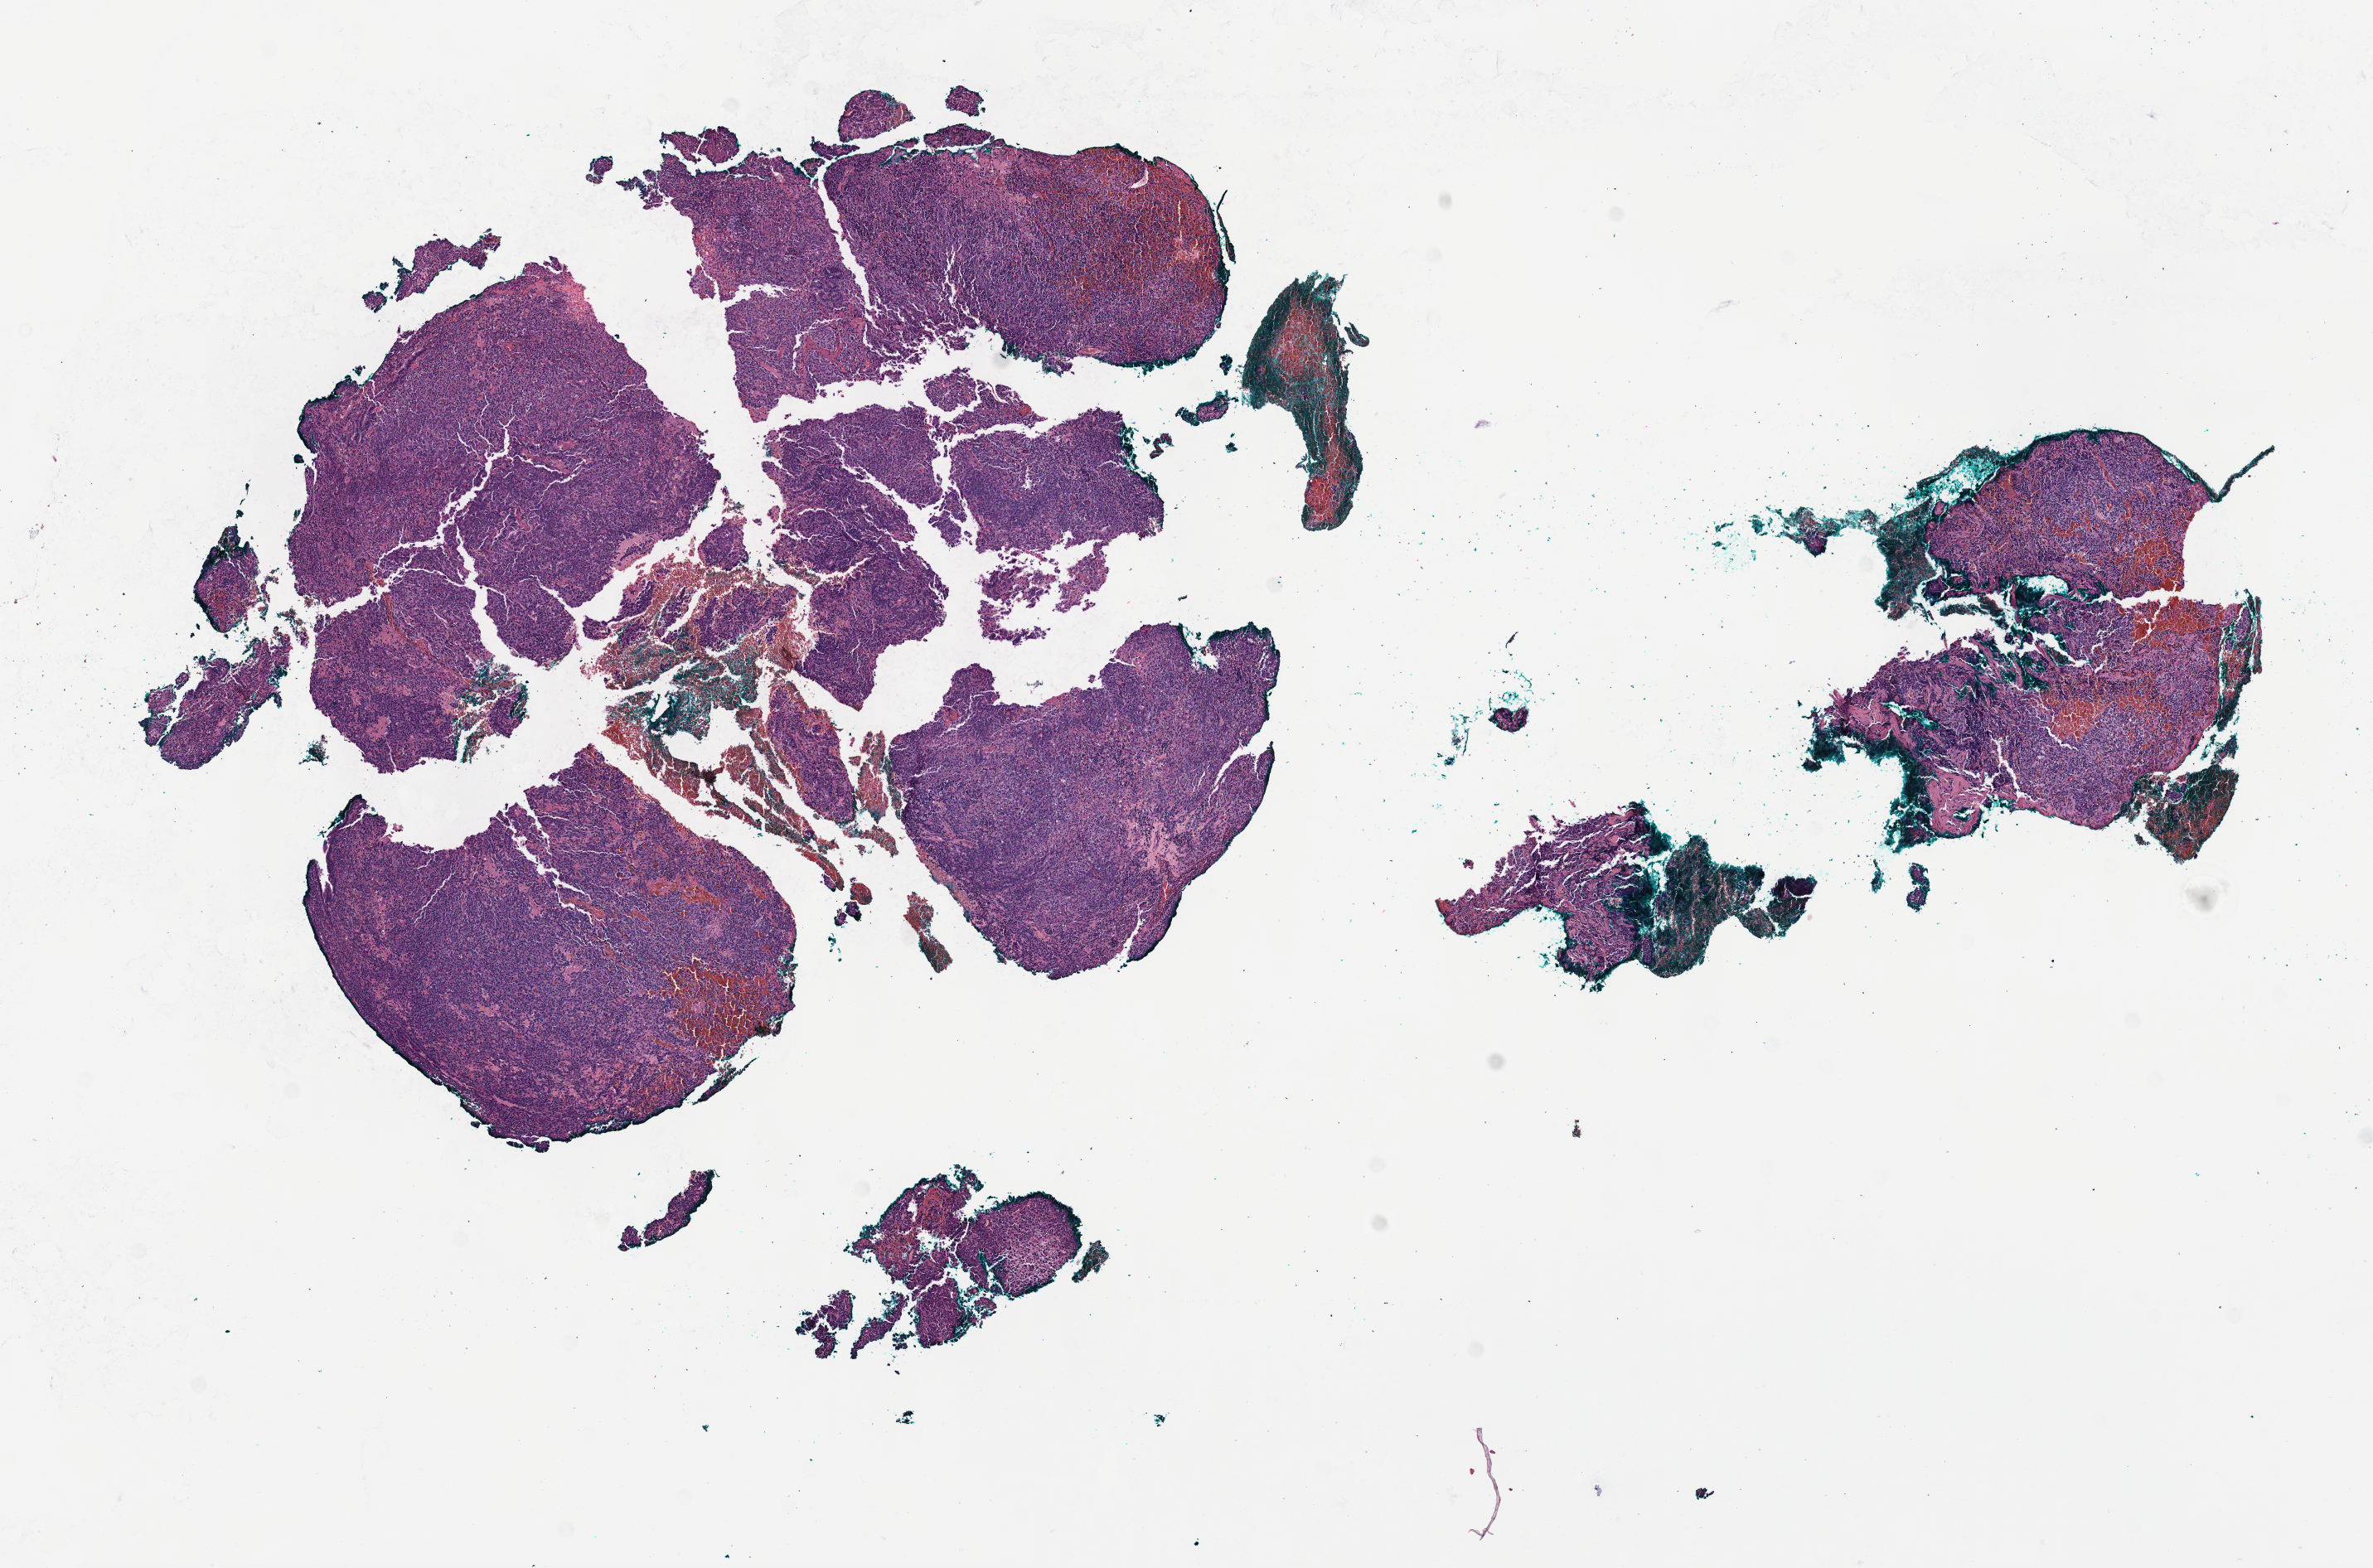
Whole-slide histology image, H&E-stained, low-resolution overview of the scanned area, about 11.6 x 7.7 mm; formalin-fixed paraffin-embedded (FFPE) diagnostic section; sample: primary tumour, cervix. Female patient; age at initial diagnosis 72 years. Histologic grade: G3 (poorly differentiated).
FIGO stage: IB. Pathologic diagnosis: Mucinous adenocarcinoma, endocervical type.